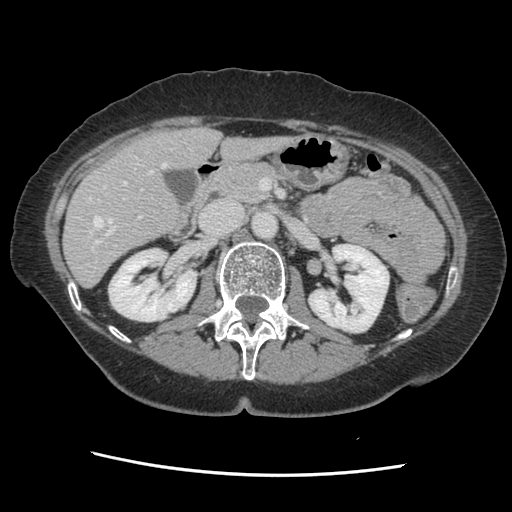
Contrast-enhanced abdominal CT, one axial slice. Slice 69 of 141 in the series (ordered by position). Soft-tissue window (W 400 / L 40 HU). 512 × 512 image matrix, field of view 330 × 330 mm. Female patient, age 61 years. From the clinical record (not read from this slice): diagnosis: colorectal cancer liver metastases, imaged before liver resection; multiple liver metastases: no; largest metastasis: 2.4 cm.
Outlined on this slice (expert manual segmentation):
- hepatic veins: bounding box (x1, y1, x2, y2) in pixels: (89, 162, 166, 228)
- liver: (64, 128, 287, 286)
- planned liver remnant (the part of the liver to remain after resection): (64, 128, 288, 286)
- portal vein (with intrahepatic branches): (91, 181, 143, 250)